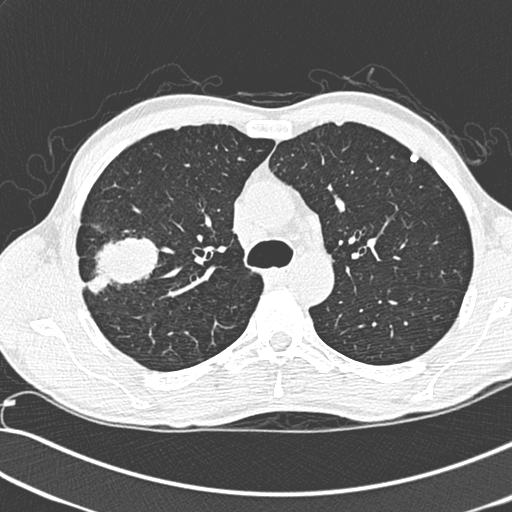
Low-dose screening chest CT, one axial slice. Position 206 of 281 along the scan axis. 120 kVp. Lung window (W 1500 / L -600 HU). 1.3 mm slice thickness. 512 × 512 image matrix, field of view 341 × 341 mm.
Outlined on this slice (expert manual segmentation):
- lesion 1 (tumor, upper lobe of right lung): bounding box <86,237,159,295> (left, top, right, bottom; pixels)